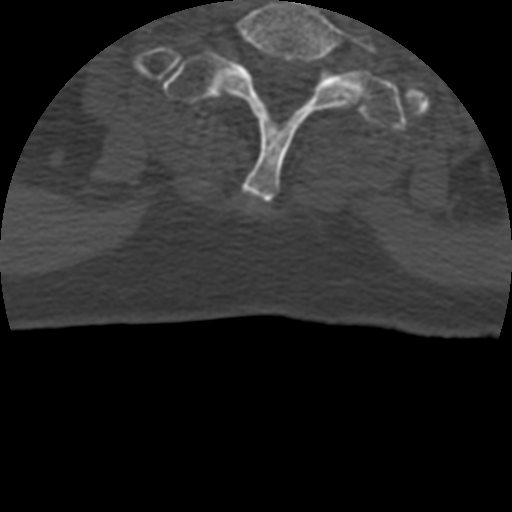
CT including the spine, one axial slice; slice 390 of 399 in the series (ordered by position); reconstruction kernel STANDARD; 120 kVp; bone window (W 1800 / L 400 HU); 1.25 mm slice thickness; 512 × 512 image matrix, field of view 160 × 160 mm. Patient age 69 years. Case-level facts recorded for this patient, not image findings: primary cancer: prostate.
Outlined on this slice (semi-automatically segmented with operator editing):
- T1 vertebra: bounding box <160,52,408,130> (left, top, right, bottom; pixels)